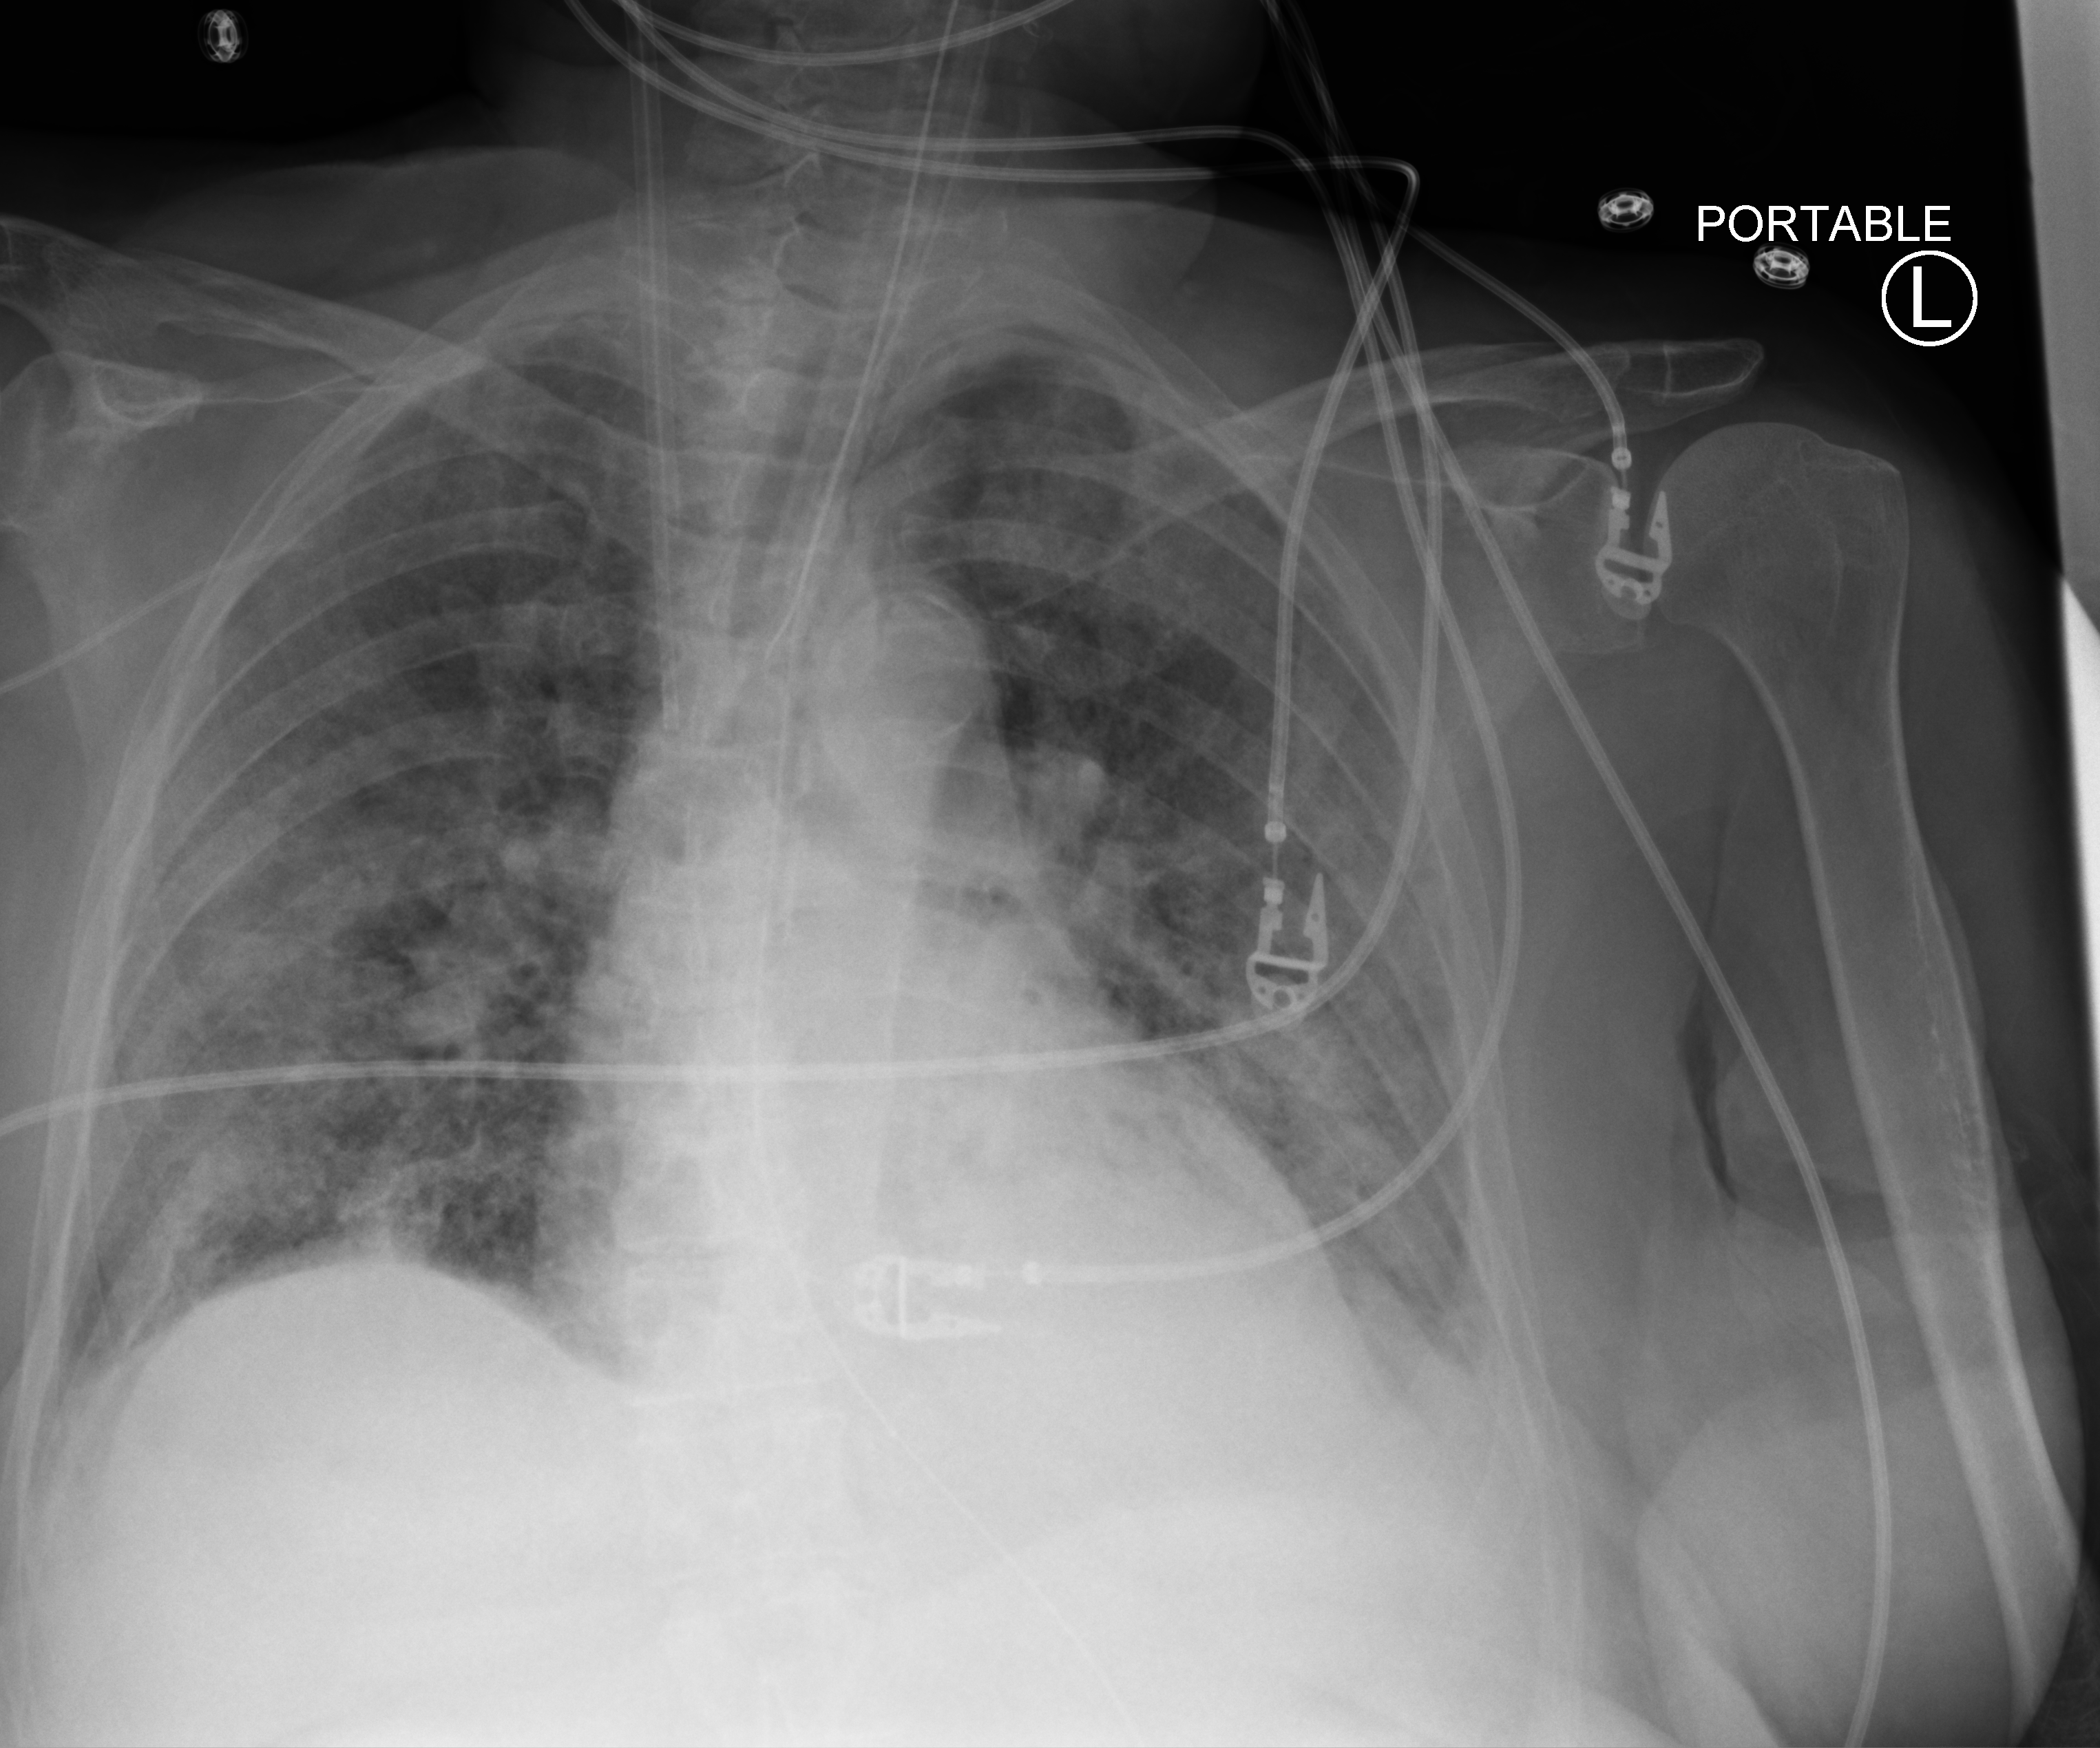
Chest X-ray (portable); anteroposterior (AP) projection. Patient hospitalised with COVID-19; female, aged 75–90 years.
From the hospital-stay record, not from the radiograph (when in the stay this image was taken is not recorded): length of hospital stay: 28 days.